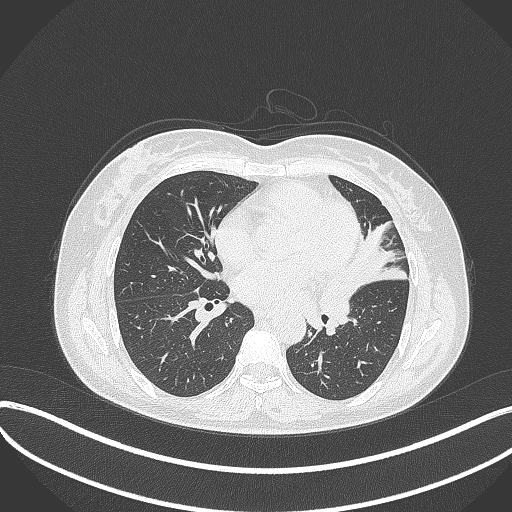
Chest CT, one axial slice. Position 166 of 373 along the scan axis. Reconstruction kernel B70f. Lung window (W 1500 / L -600 HU). 1 mm slice thickness. 512 × 512 image matrix, field of view 400 × 400 mm. Female patient, age 54 years. From the clinical record (not read from this slice): clinical TNM (as recorded): T2a N1 M0.
Annotated regions visible in this slice (rectangle marked by the reading radiologist):
- lung tumour (recorded histology: small cell carcinoma): bounding box (x1, y1, x2, y2) in pixels: (313, 260, 365, 333)